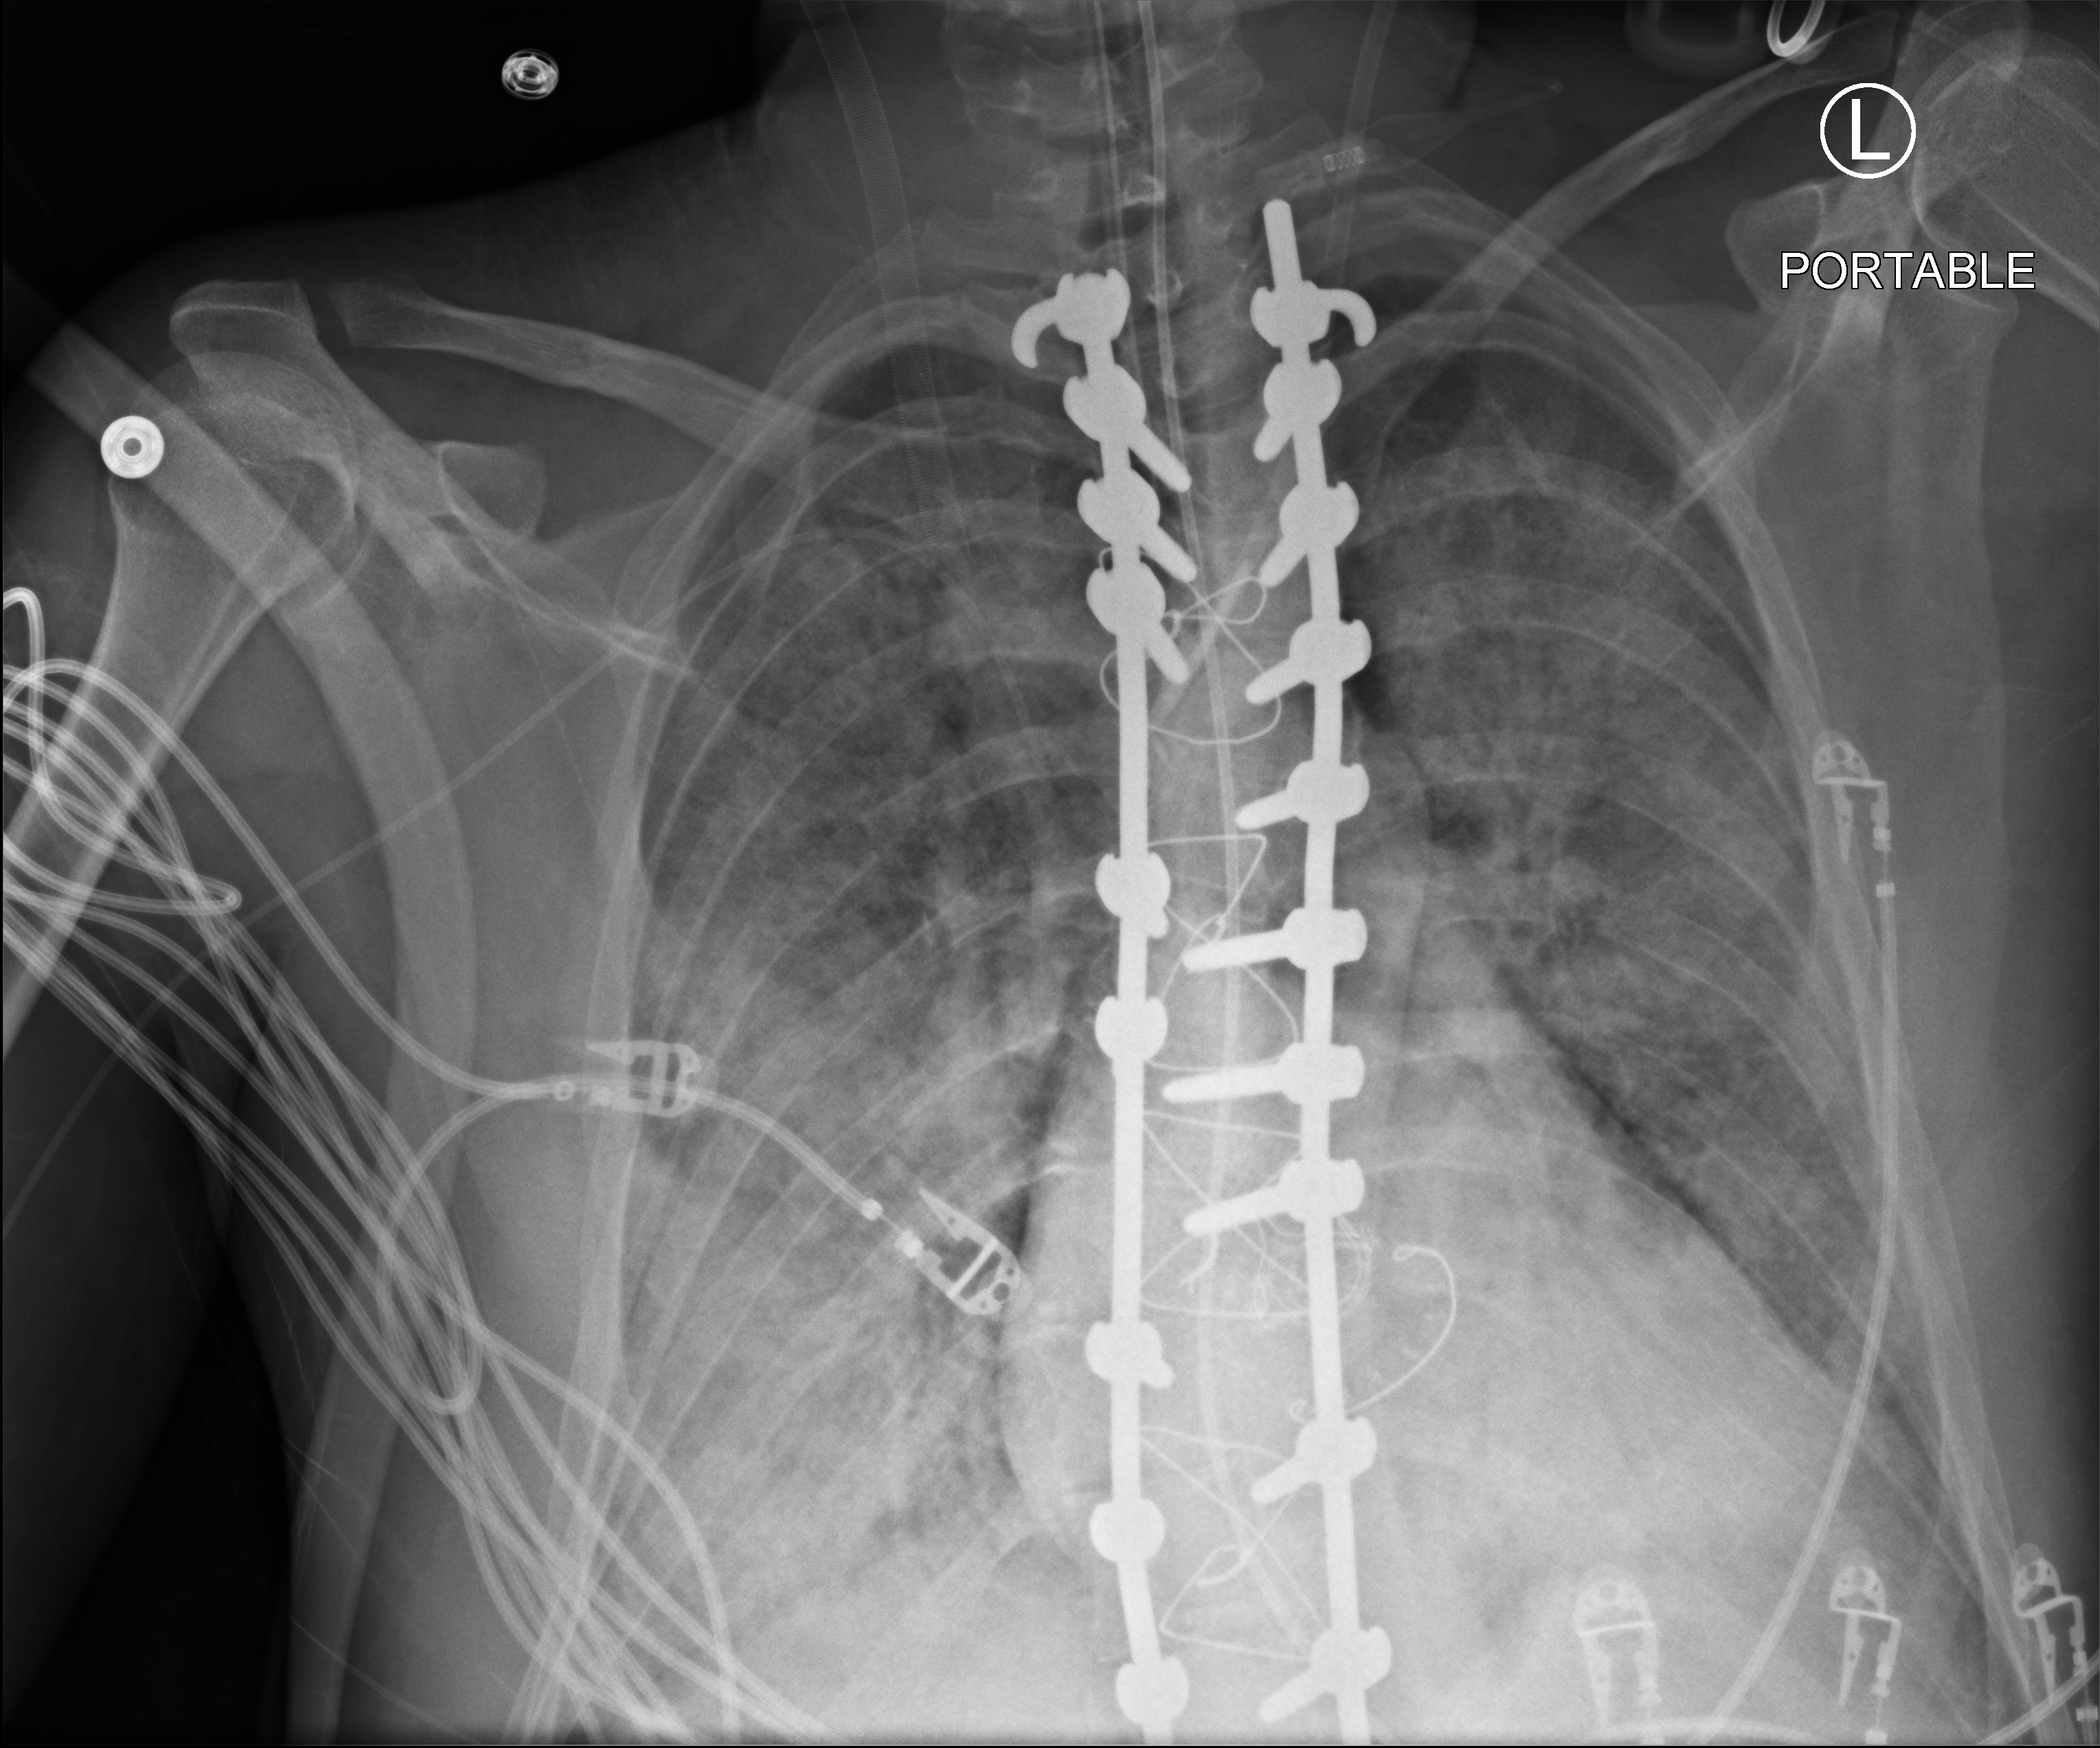
Portable chest radiograph, anteroposterior (AP) projection. Patient hospitalised with COVID-19, aged 18–59 years.
Admission-level facts for this patient (not findings on this image; timing relative to this image not recorded): admitted to intensive care during this hospital stay: yes; length of hospital stay: 15 days; mechanically ventilated during this hospital stay: yes.